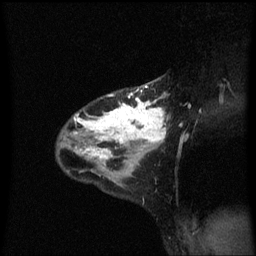
Breast MRI (dynamic contrast-enhanced), one sagittal slice; position 41 of 60 along the scan axis; dynamic contrast-enhanced series, image 2 of 3 at this slice position (ordered by acquisition); 1.5 T; TE 4.2 ms, TR 8.4 ms; 2 mm slice thickness; 256 × 256 image matrix. Patient: female, 32 years.
Annotated regions visible in this slice (semi-automatically segmented with operator editing):
- analysis volume of interest (the breast-tissue region the enhancement analysis was run in; not a lesion): bounding box [x1, y1, x2, y2] px = [58, 78, 170, 167]
- tumour enhancement mask (voxels above the 70 % enhancement threshold inside the analysis volume of interest): [71, 86, 167, 159]